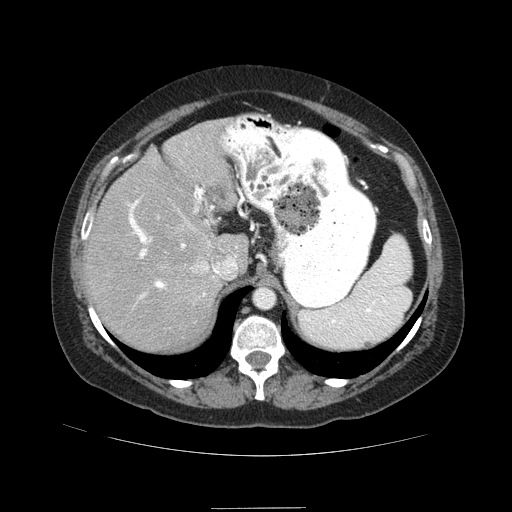
Contrast-enhanced abdominal CT (liver protocol), one axial slice; reconstruction kernel STANDARD; 120 kVp; soft-tissue window (W 400 / L 40 HU); 2.5 mm slice thickness; 512 × 512 image matrix, field of view 400 × 400 mm. From the clinical record (not read from this slice): diagnosis: hepatocellular carcinoma (patient treated with transarterial chemoembolisation; whether this scan precedes or follows treatment is not stated here); TNM stage (as recorded): Stage-IIIB; Child-Pugh class: A; tumour nodularity: multinodular.
Annotated regions visible in this slice (semi-automatic segmentation, software-assisted and operator-edited):
- abdominal aorta: bounding box <255,288,275,308> (left, top, right, bottom; pixels)
- liver parenchyma outside the tumour (the mass and vessels are separate outlines, so this box may not span the whole liver): <84,118,248,352>
- liver vessels: <87,186,237,299>